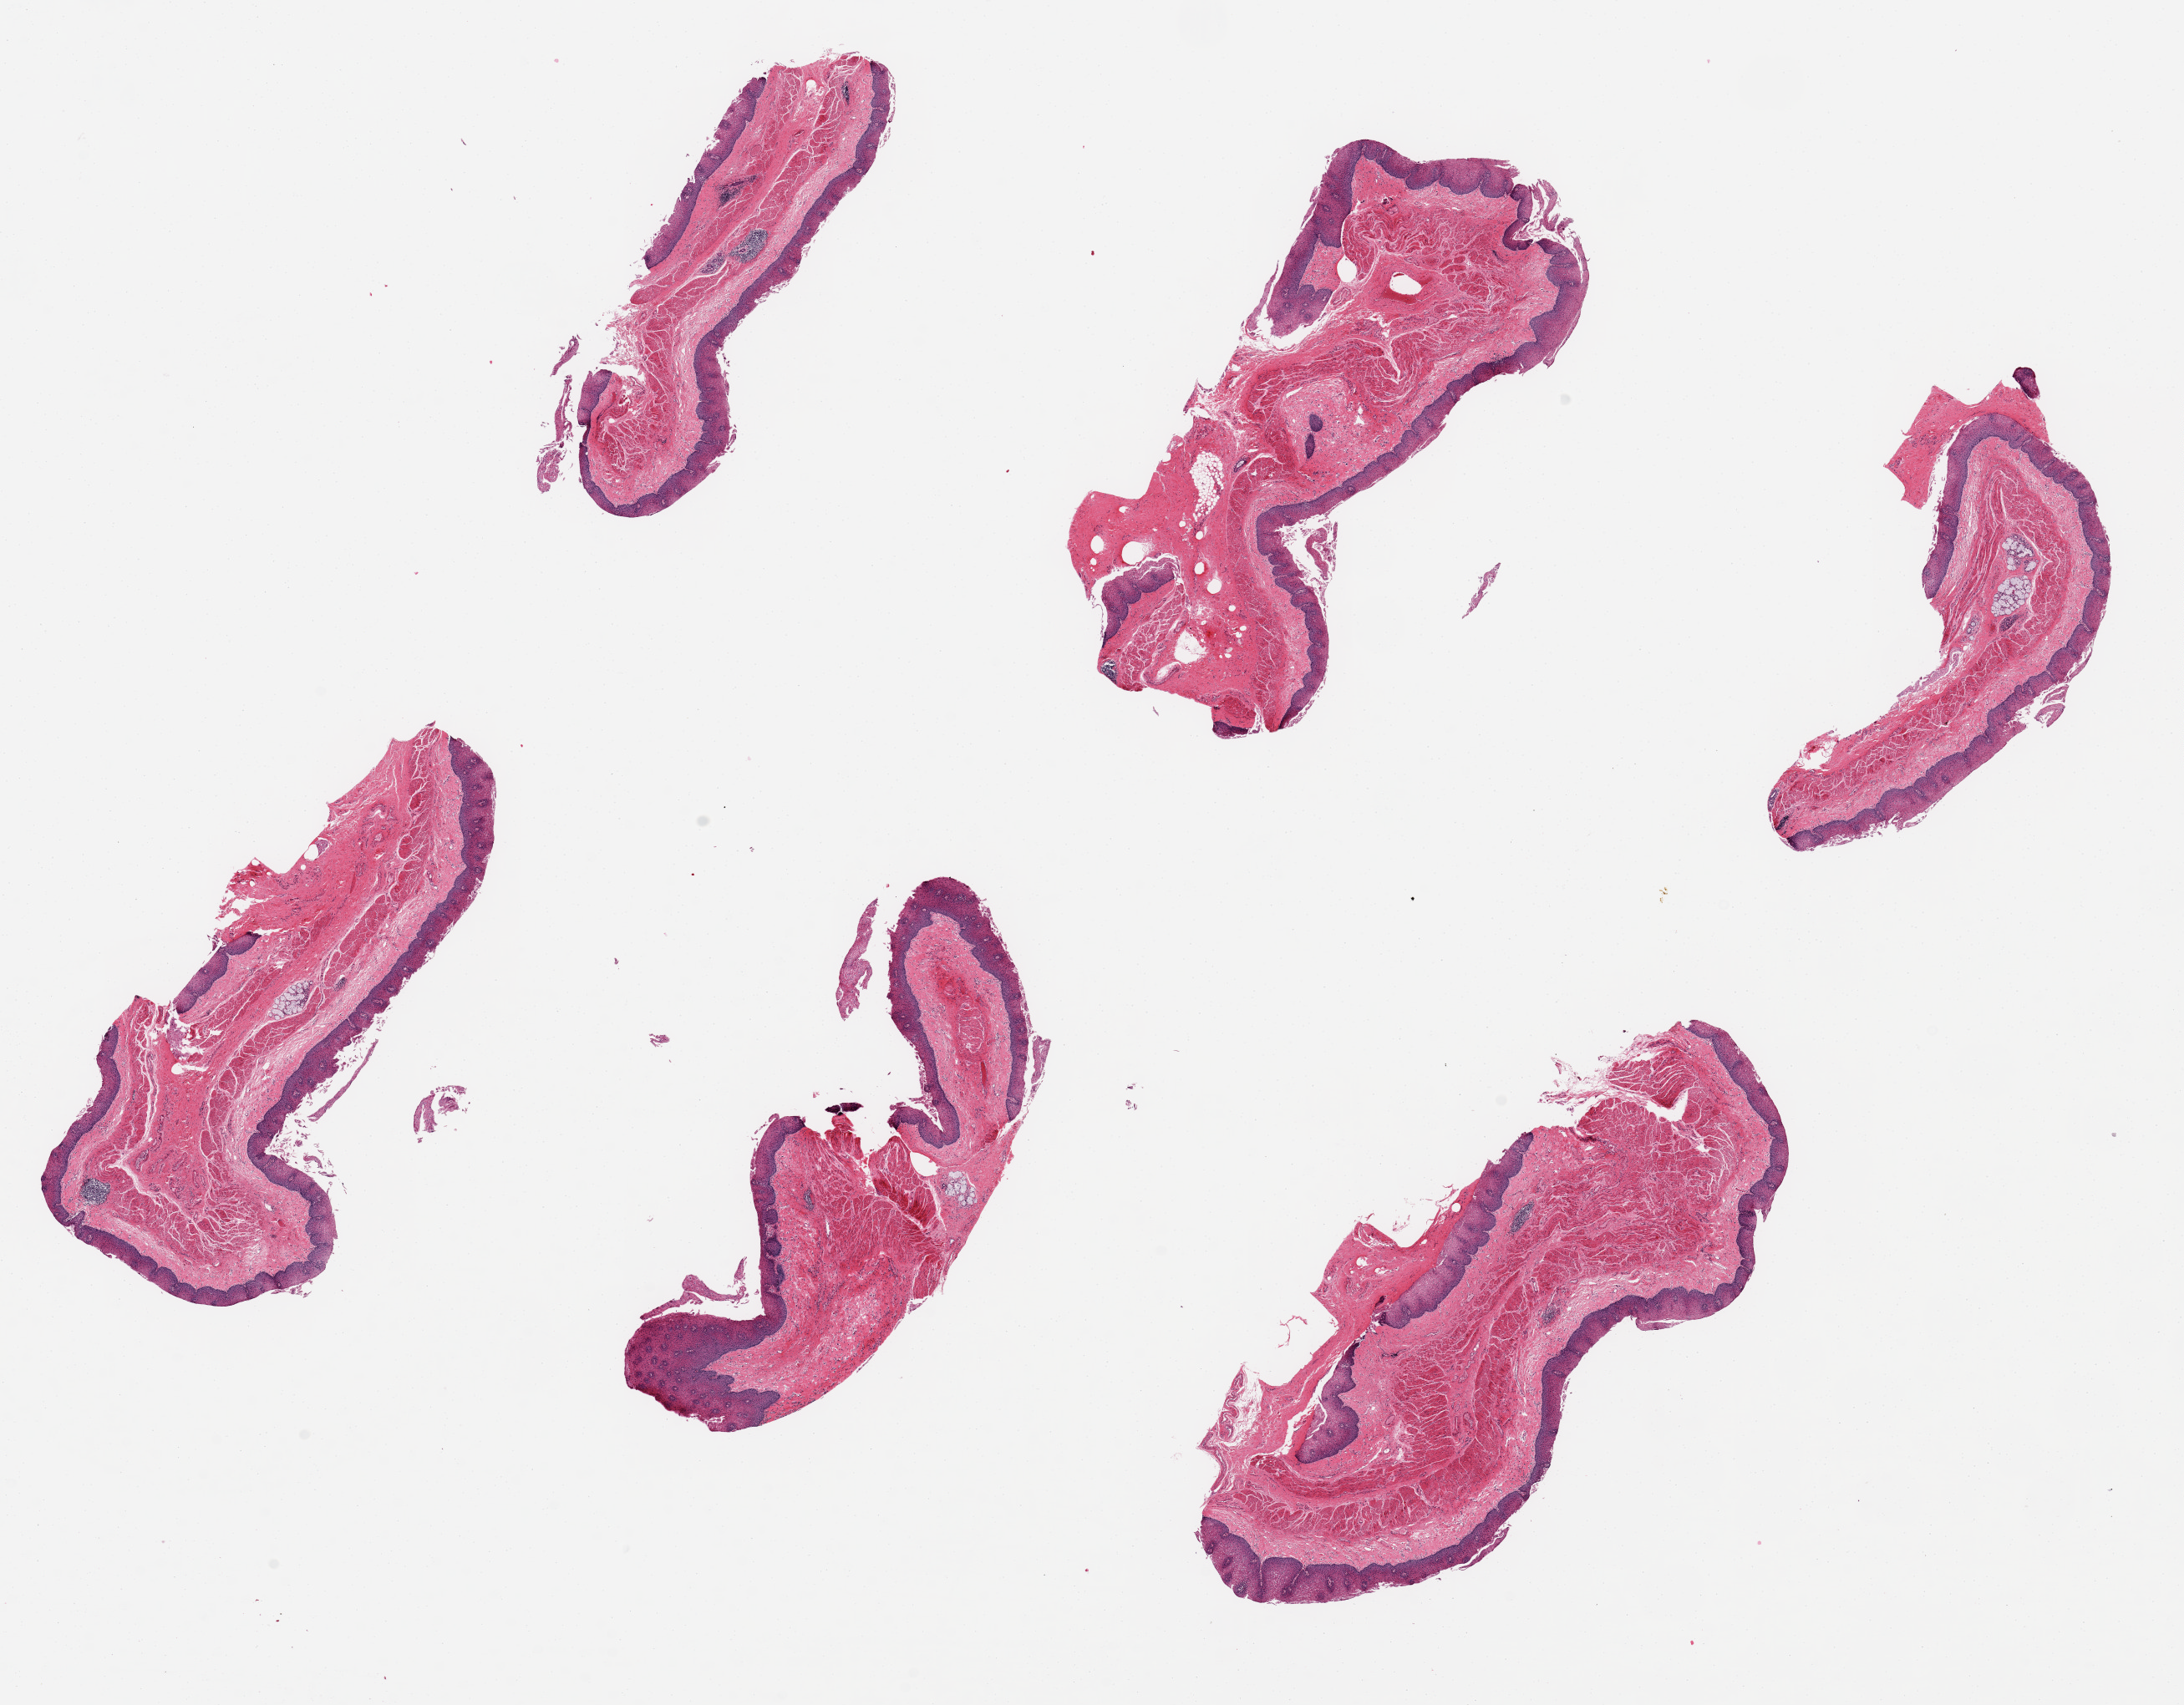
Digitized haematoxylin and eosin-stained section, shown as a low-resolution overview of the whole scanned area (about 20.7 x 16.1 mm, slide scanned at 20x). PAXgene-fixed paraffin-embedded (PFPE) section. Target tissue: esophageal mucous membrane. Tissue donor sample.
* review note (as recorded): 6 pieces up to 7x3 mm